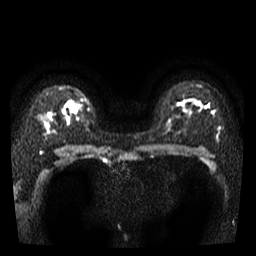
Breast MRI, one axial slice; position 25 of 40 along the scan axis; diffusion-weighted series; image 2 of 4 stored at this slice position (different b-values; order by instance number); 3 T; 256 × 256 image matrix, field of view 280 × 280 mm. Female patient.
Annotated regions visible in this slice (expert manual segmentation):
- tumour on diffusion-weighted imaging: bounding box <73,106,76,110> (left, top, right, bottom; pixels)